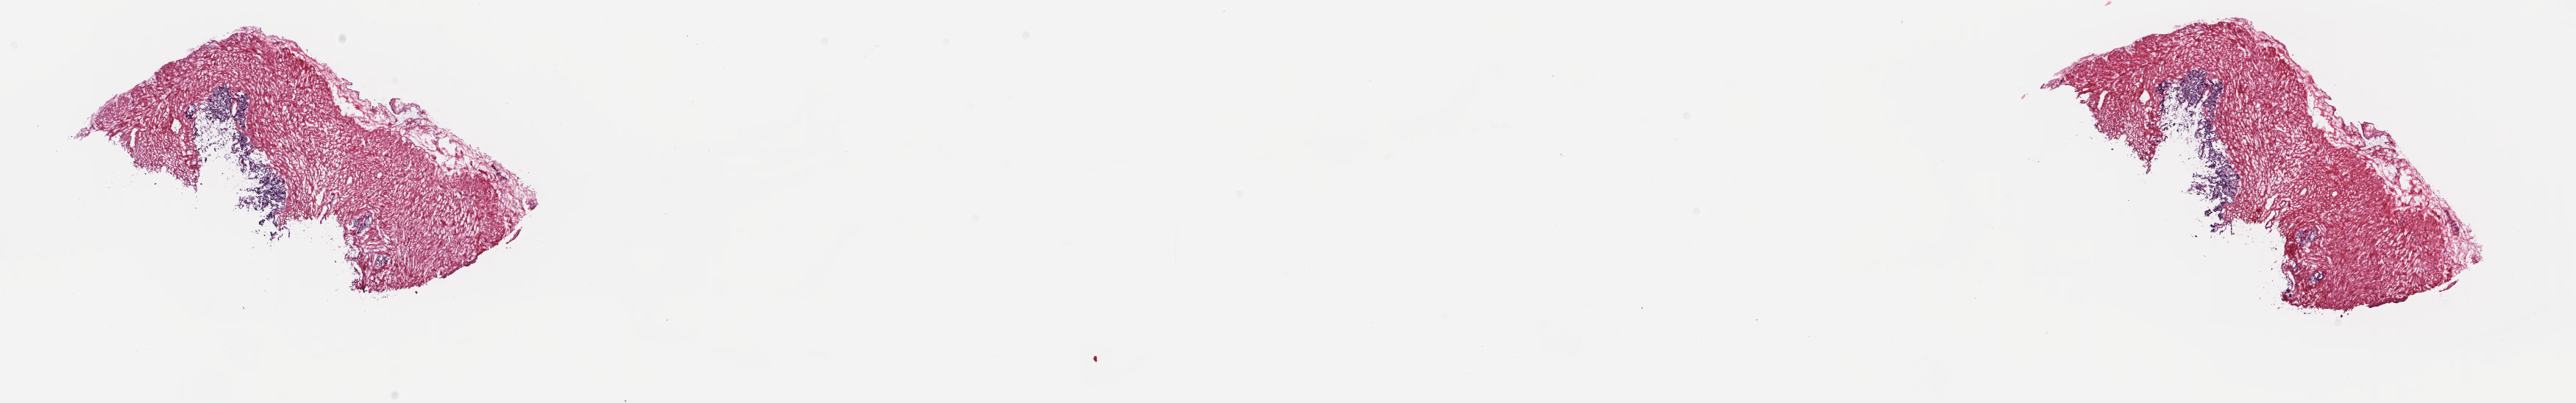
Whole-slide histology image, H&E-stained — whole scanned area (about 27.8 x 4.3 mm) shown as a low-resolution overview. Frozen section from the top of the tissue portion. Sample: solid tissue normal (non-tumour tissue), prostate. Patient: male, age at initial diagnosis 64 years. Pathologist review of this section (percent, as recorded): tumour cells 0%, tumour nuclei 0%.
This section: solid tissue normal sample (biorepository sample class). Patient diagnosis: Adenocarcinoma, NOS (prostate gland).